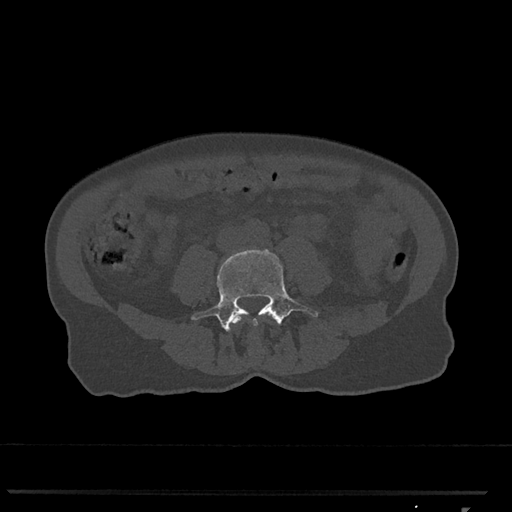
CT including the spine, one axial slice; position 223 of 793 along the scan axis; 120 kVp; bone window (W 1800 / L 400 HU); 0.5 mm slice thickness; 512 × 512 image matrix, field of view 380 × 380 mm. Patient: female, 62 years. From the clinical record (not read from this slice): primary cancer: renal.
Outlined on this slice (semi-automatic segmentation, software-assisted and operator-edited):
- L3 vertebra: box from (x=233, y=314) to (x=271, y=325) px
- L4 vertebra: (x=191, y=249)–(x=318, y=332)